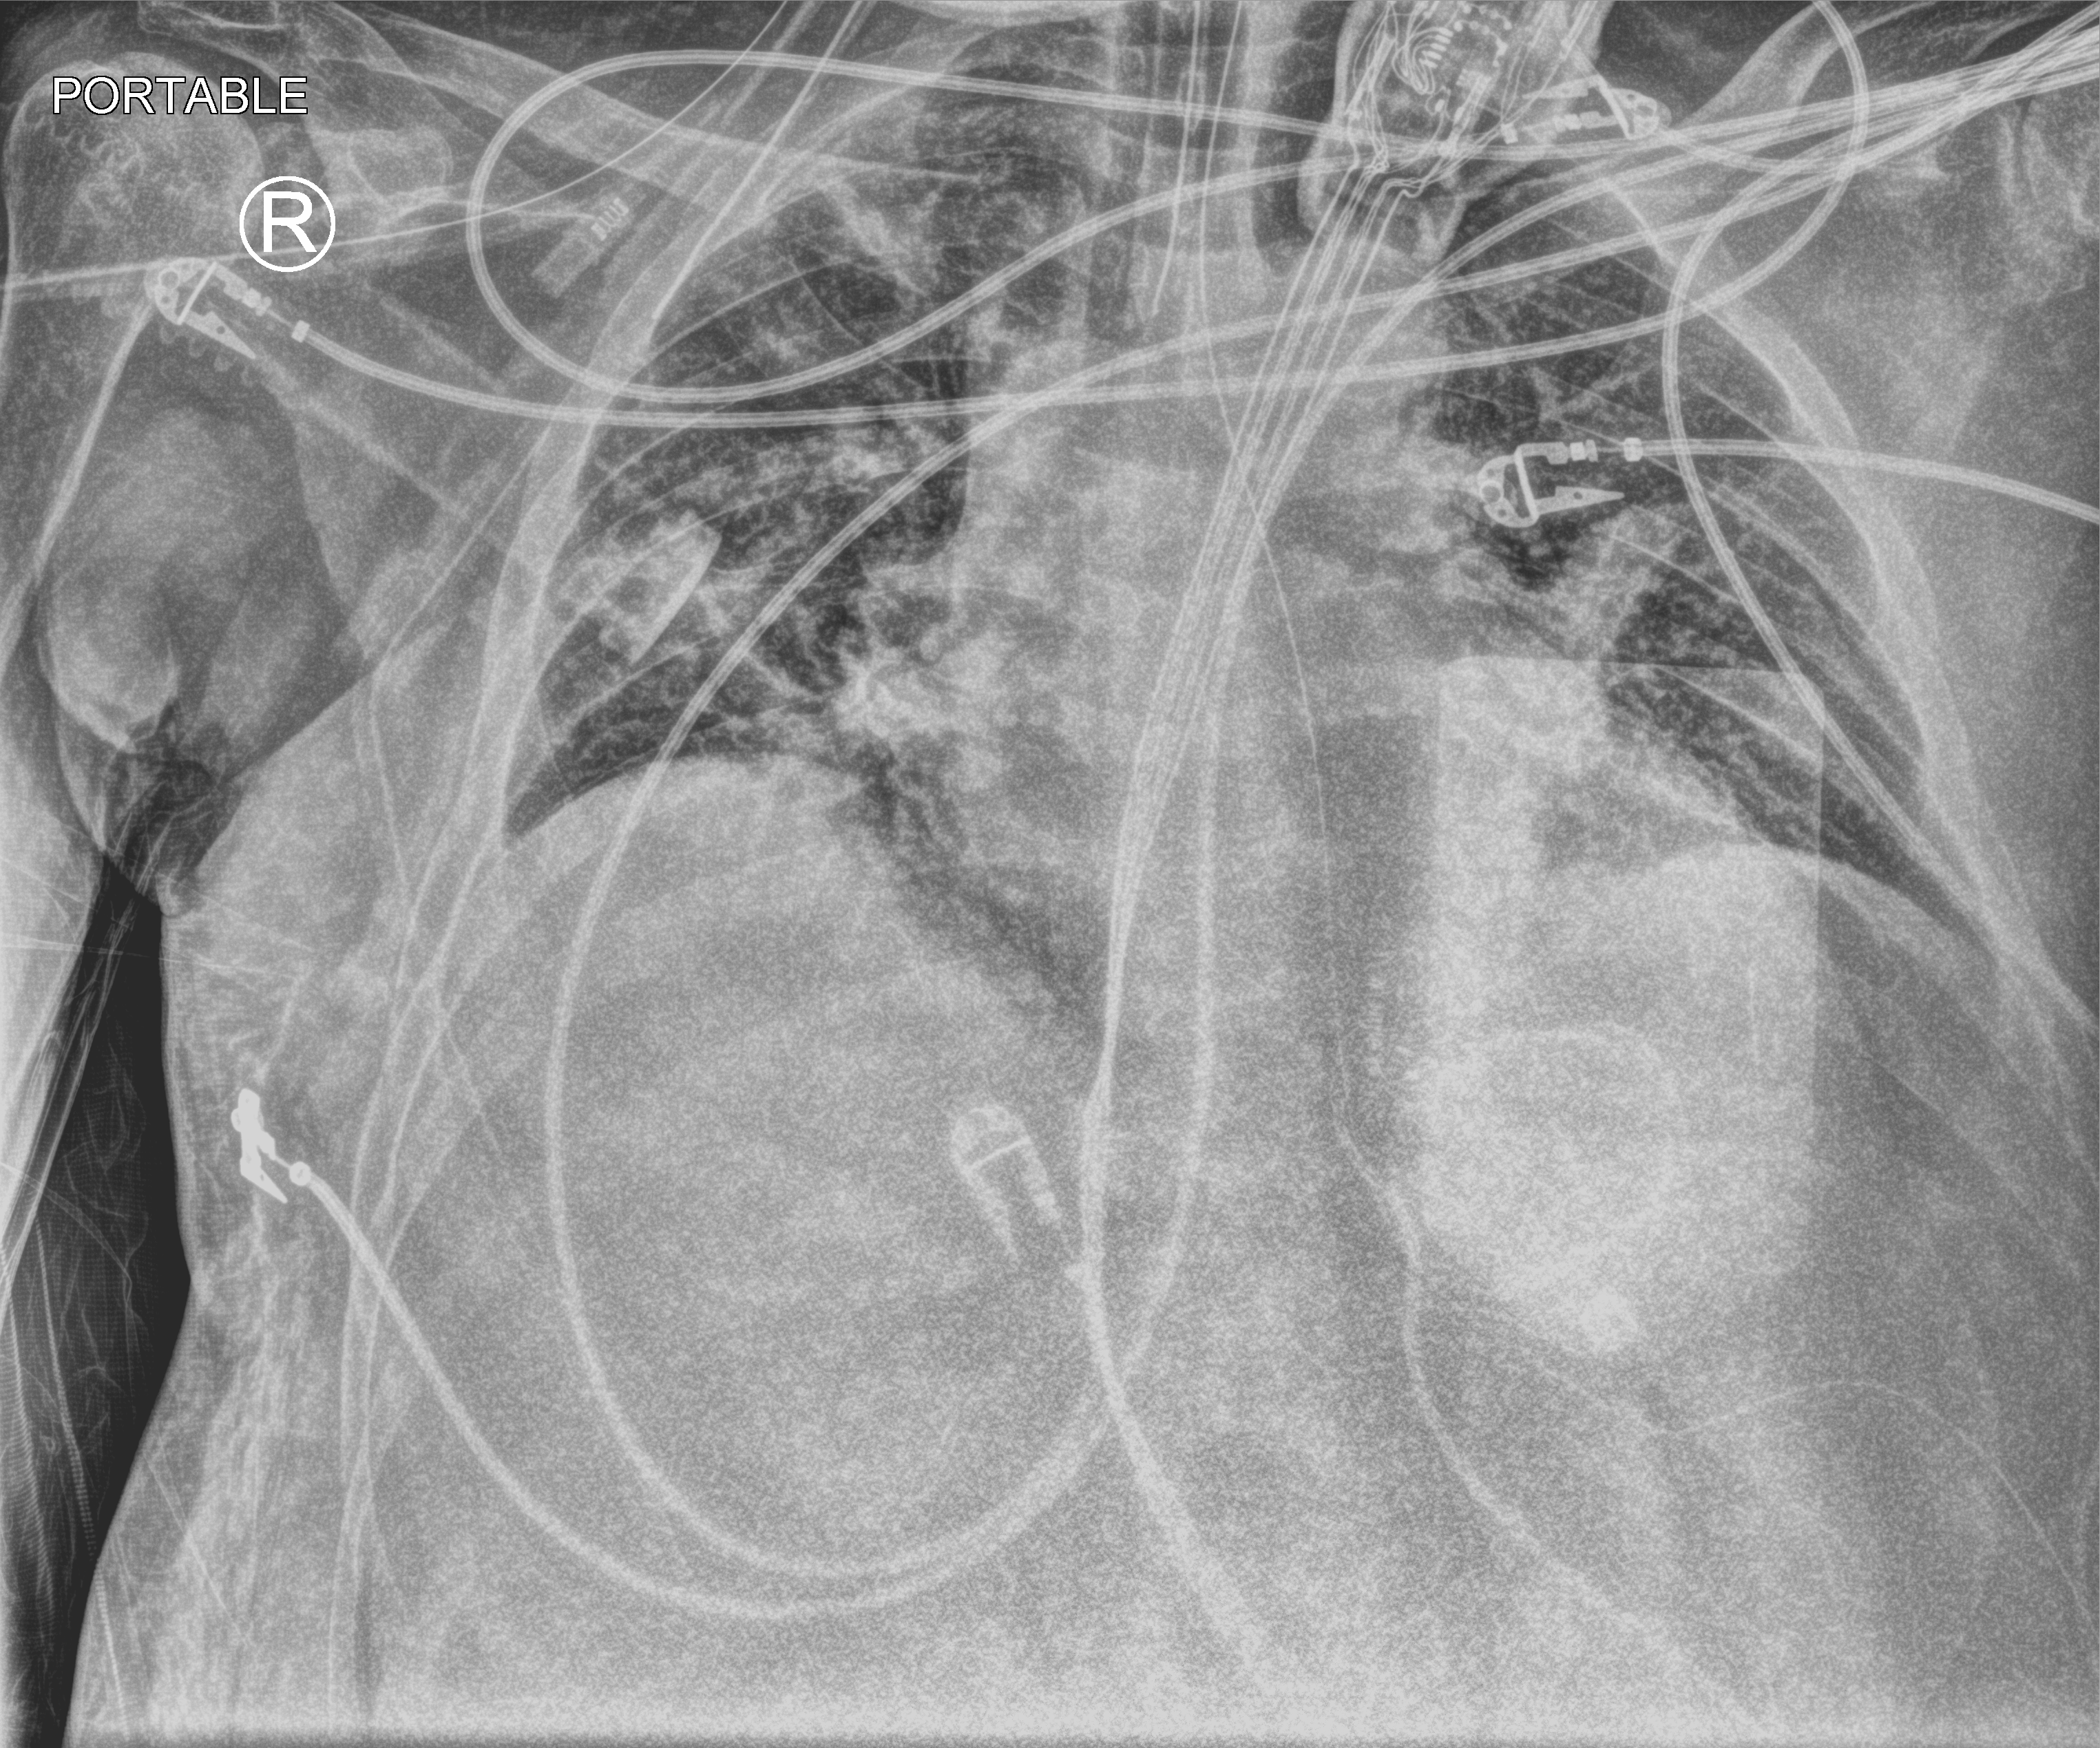
Bedside chest radiograph (computed radiography), anteroposterior (AP) projection. Patient hospitalised with COVID-19; male, aged 60–74 years.
Hospital-stay facts (about this admission, not read from this image; timing relative to this image not recorded): admitted to intensive care during this hospital stay: yes.